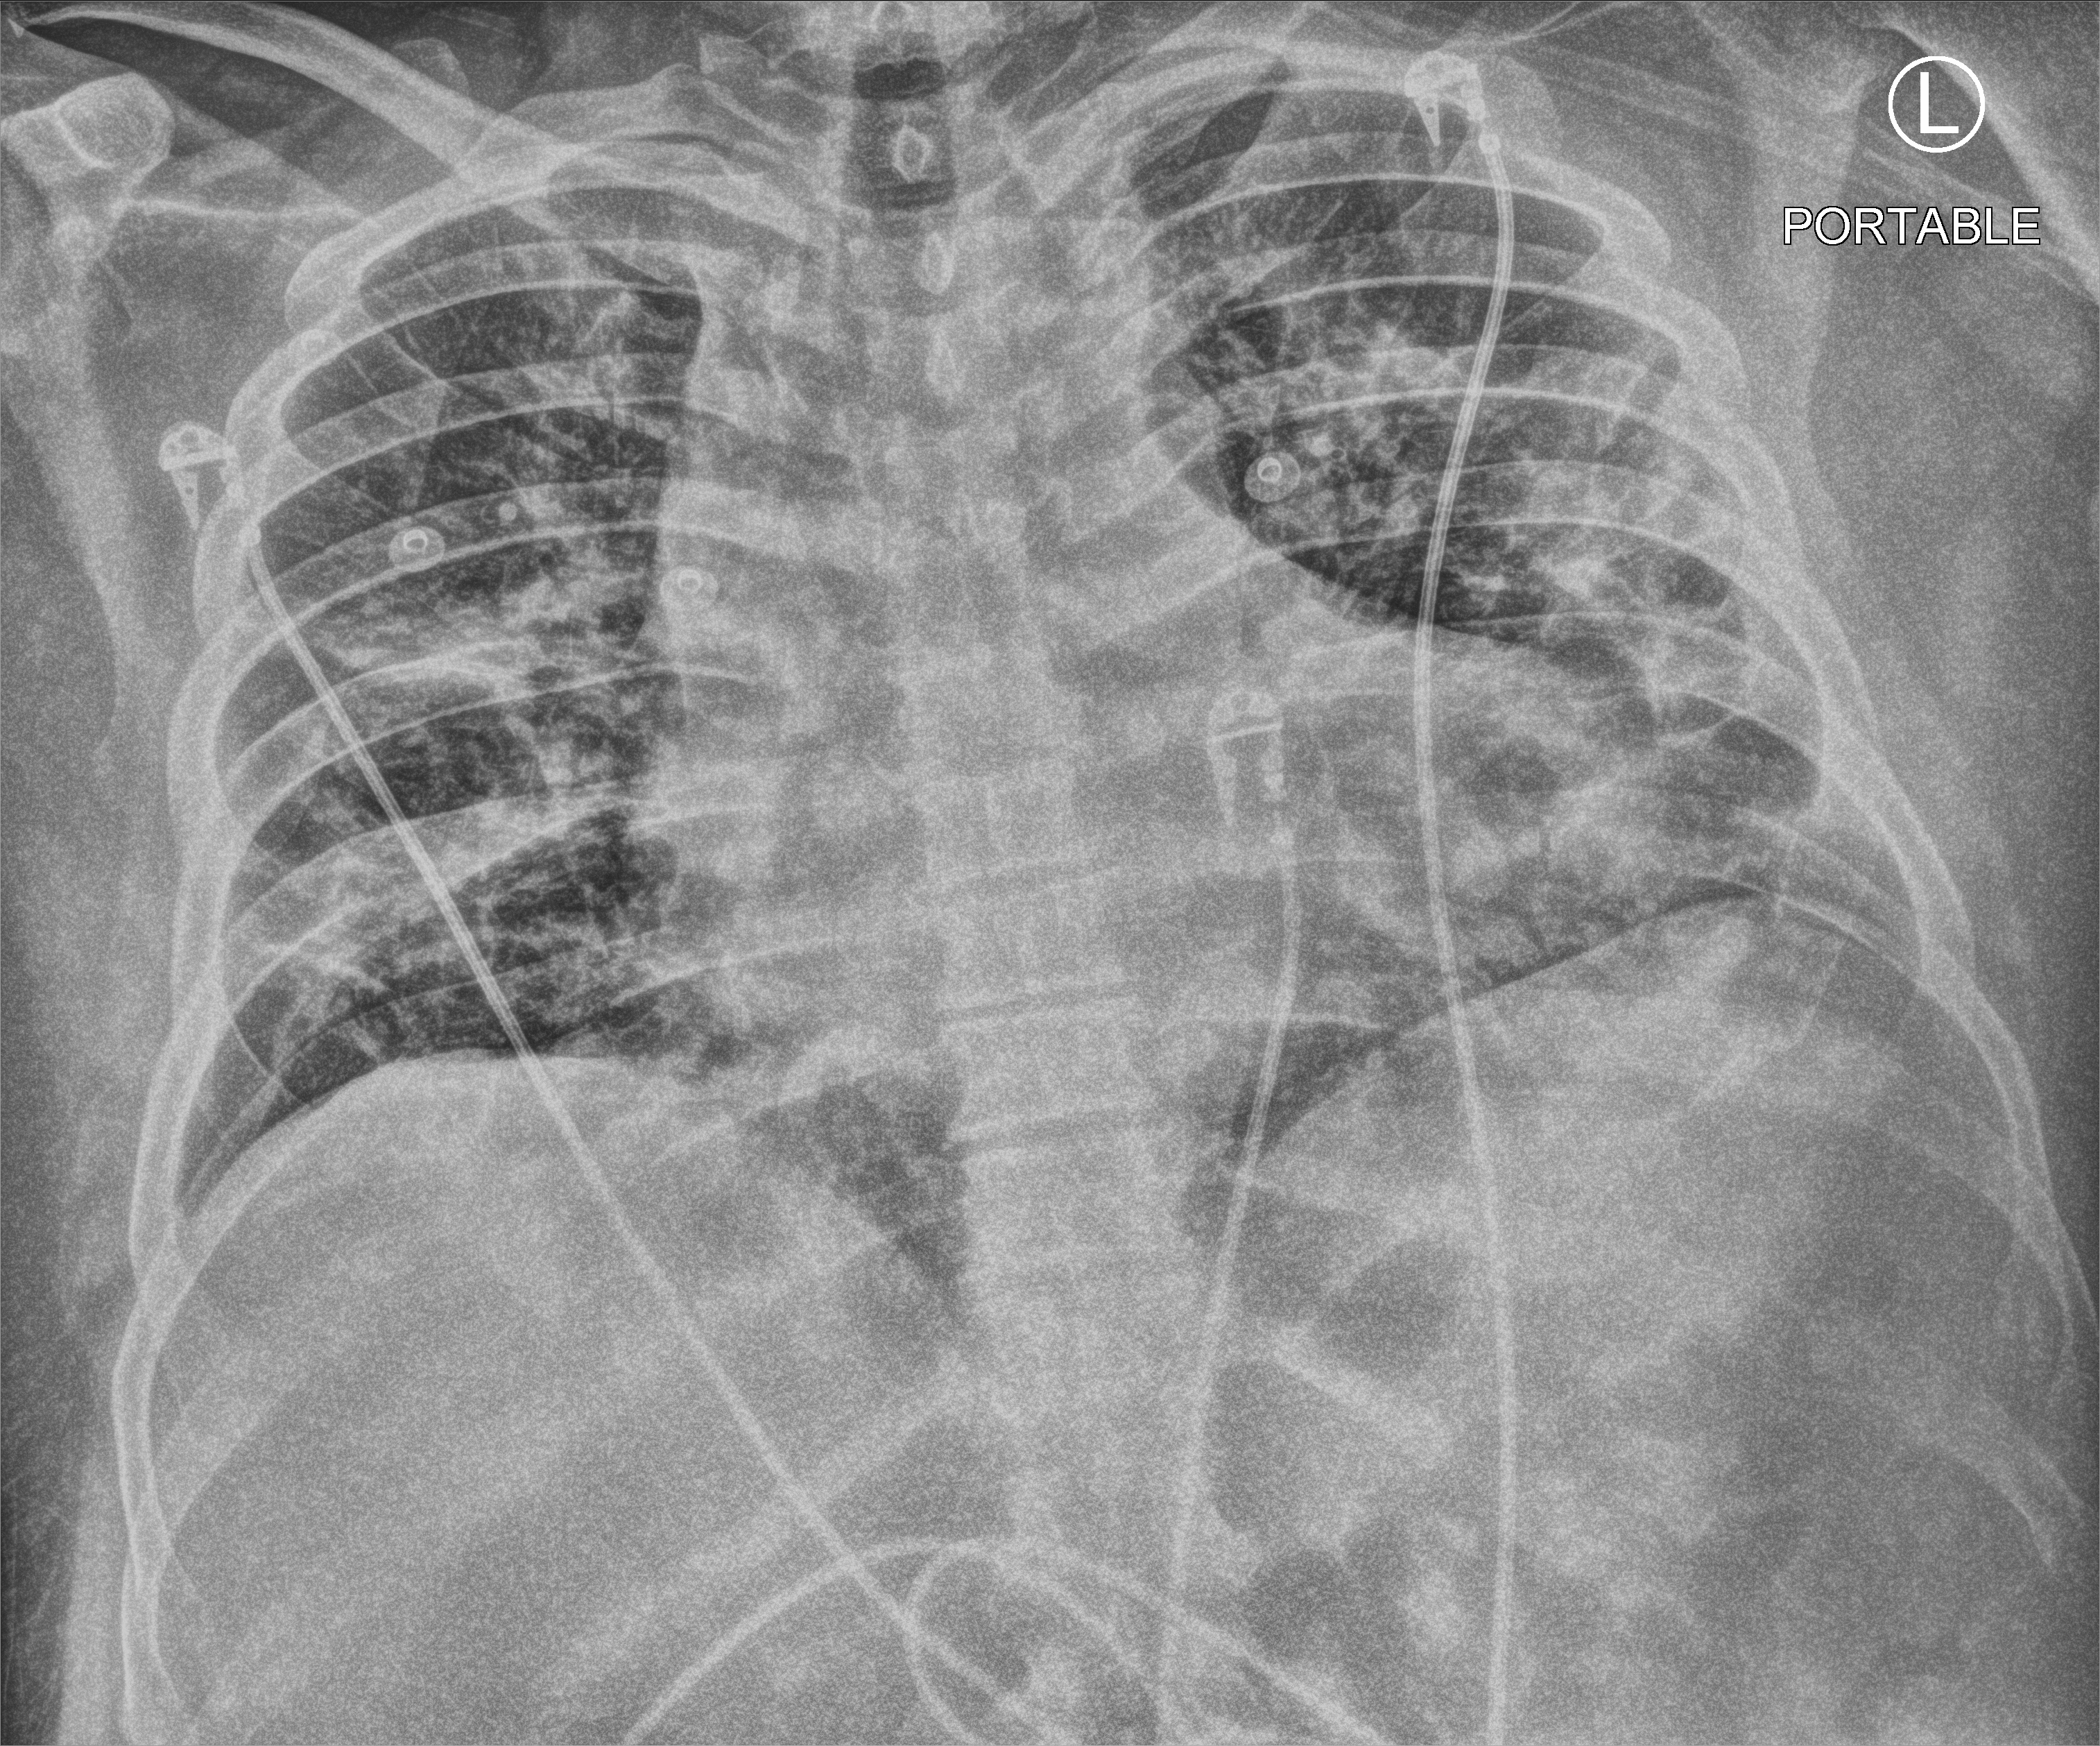
Bedside chest radiograph (computed radiography), anteroposterior (AP) projection. Patient hospitalised with COVID-19; male, aged 18–59 years.
From the hospital-stay record, not from the radiograph (when in the stay this image was taken is not recorded): admitted to intensive care during this hospital stay: no; mechanically ventilated during this hospital stay: no; diabetes (admission record): no.